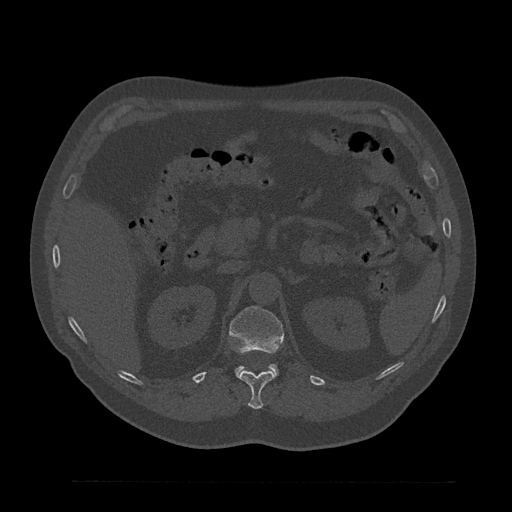
CT including the spine, one axial slice. Slice 200 of 797 in the series (ordered by position). Reconstruction kernel Br40s/3. Bone window (W 1800 / L 400 HU). 512 × 512 image matrix. Male patient, age 61 years. Case-level facts recorded for this patient, not image findings: primary cancer: prostate.
Annotated regions visible in this slice (semi-automatic segmentation, software-assisted and operator-edited):
- L1 vertebra: box from (x=230, y=306) to (x=284, y=376) px
- T12 vertebra: (x=238, y=371)–(x=275, y=409)